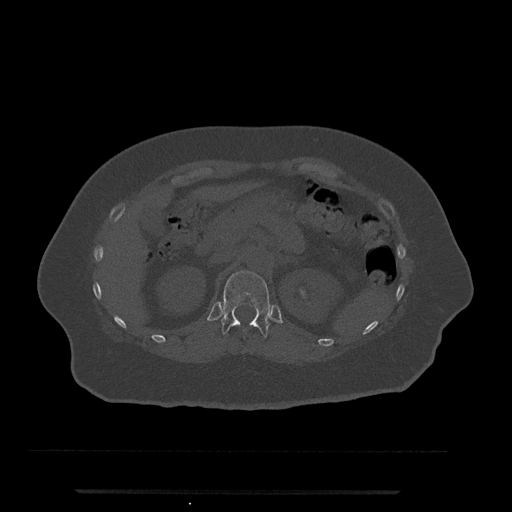
CT including the spine, one axial slice; 120 kVp; bone window (W 1800 / L 400 HU); 0.5 mm slice thickness; 512 × 512 image matrix. Female patient, age 51 years. From the clinical record (not read from this slice): primary cancer: neuro; vertebrae with lytic lesions (as recorded): T8.
Outlined on this slice (semi-automatic segmentation, software-assisted and operator-edited):
- T12 vertebra: bounding box [x1, y1, x2, y2] px = [221, 271, 271, 338]